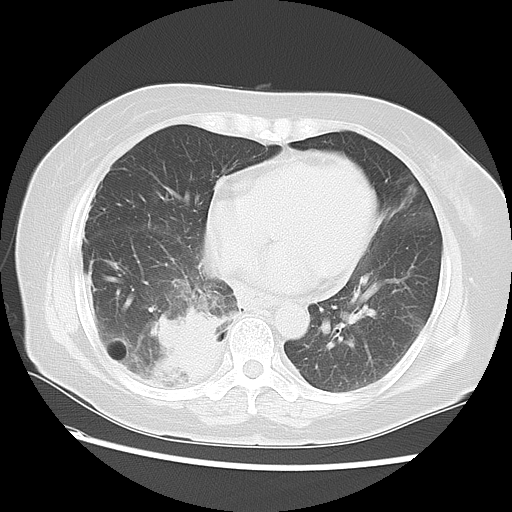
Chest CT, one axial slice. Position 25 of 57 along the scan axis. Reconstruction kernel LUNG. Lung window (W 1500 / L -600 HU). 5 mm slice thickness. 512 × 512 image matrix, field of view 350 × 350 mm. Patient: female, 69 years. Case-level facts recorded for this patient, not image findings: clinical TNM (as recorded): T2 N1 M1a.
Outlined on this slice (rectangle marked by the reading radiologist):
- lung tumour (recorded histology: adenocarcinoma): bounding box (x1, y1, x2, y2) in pixels: (147, 296, 237, 386)